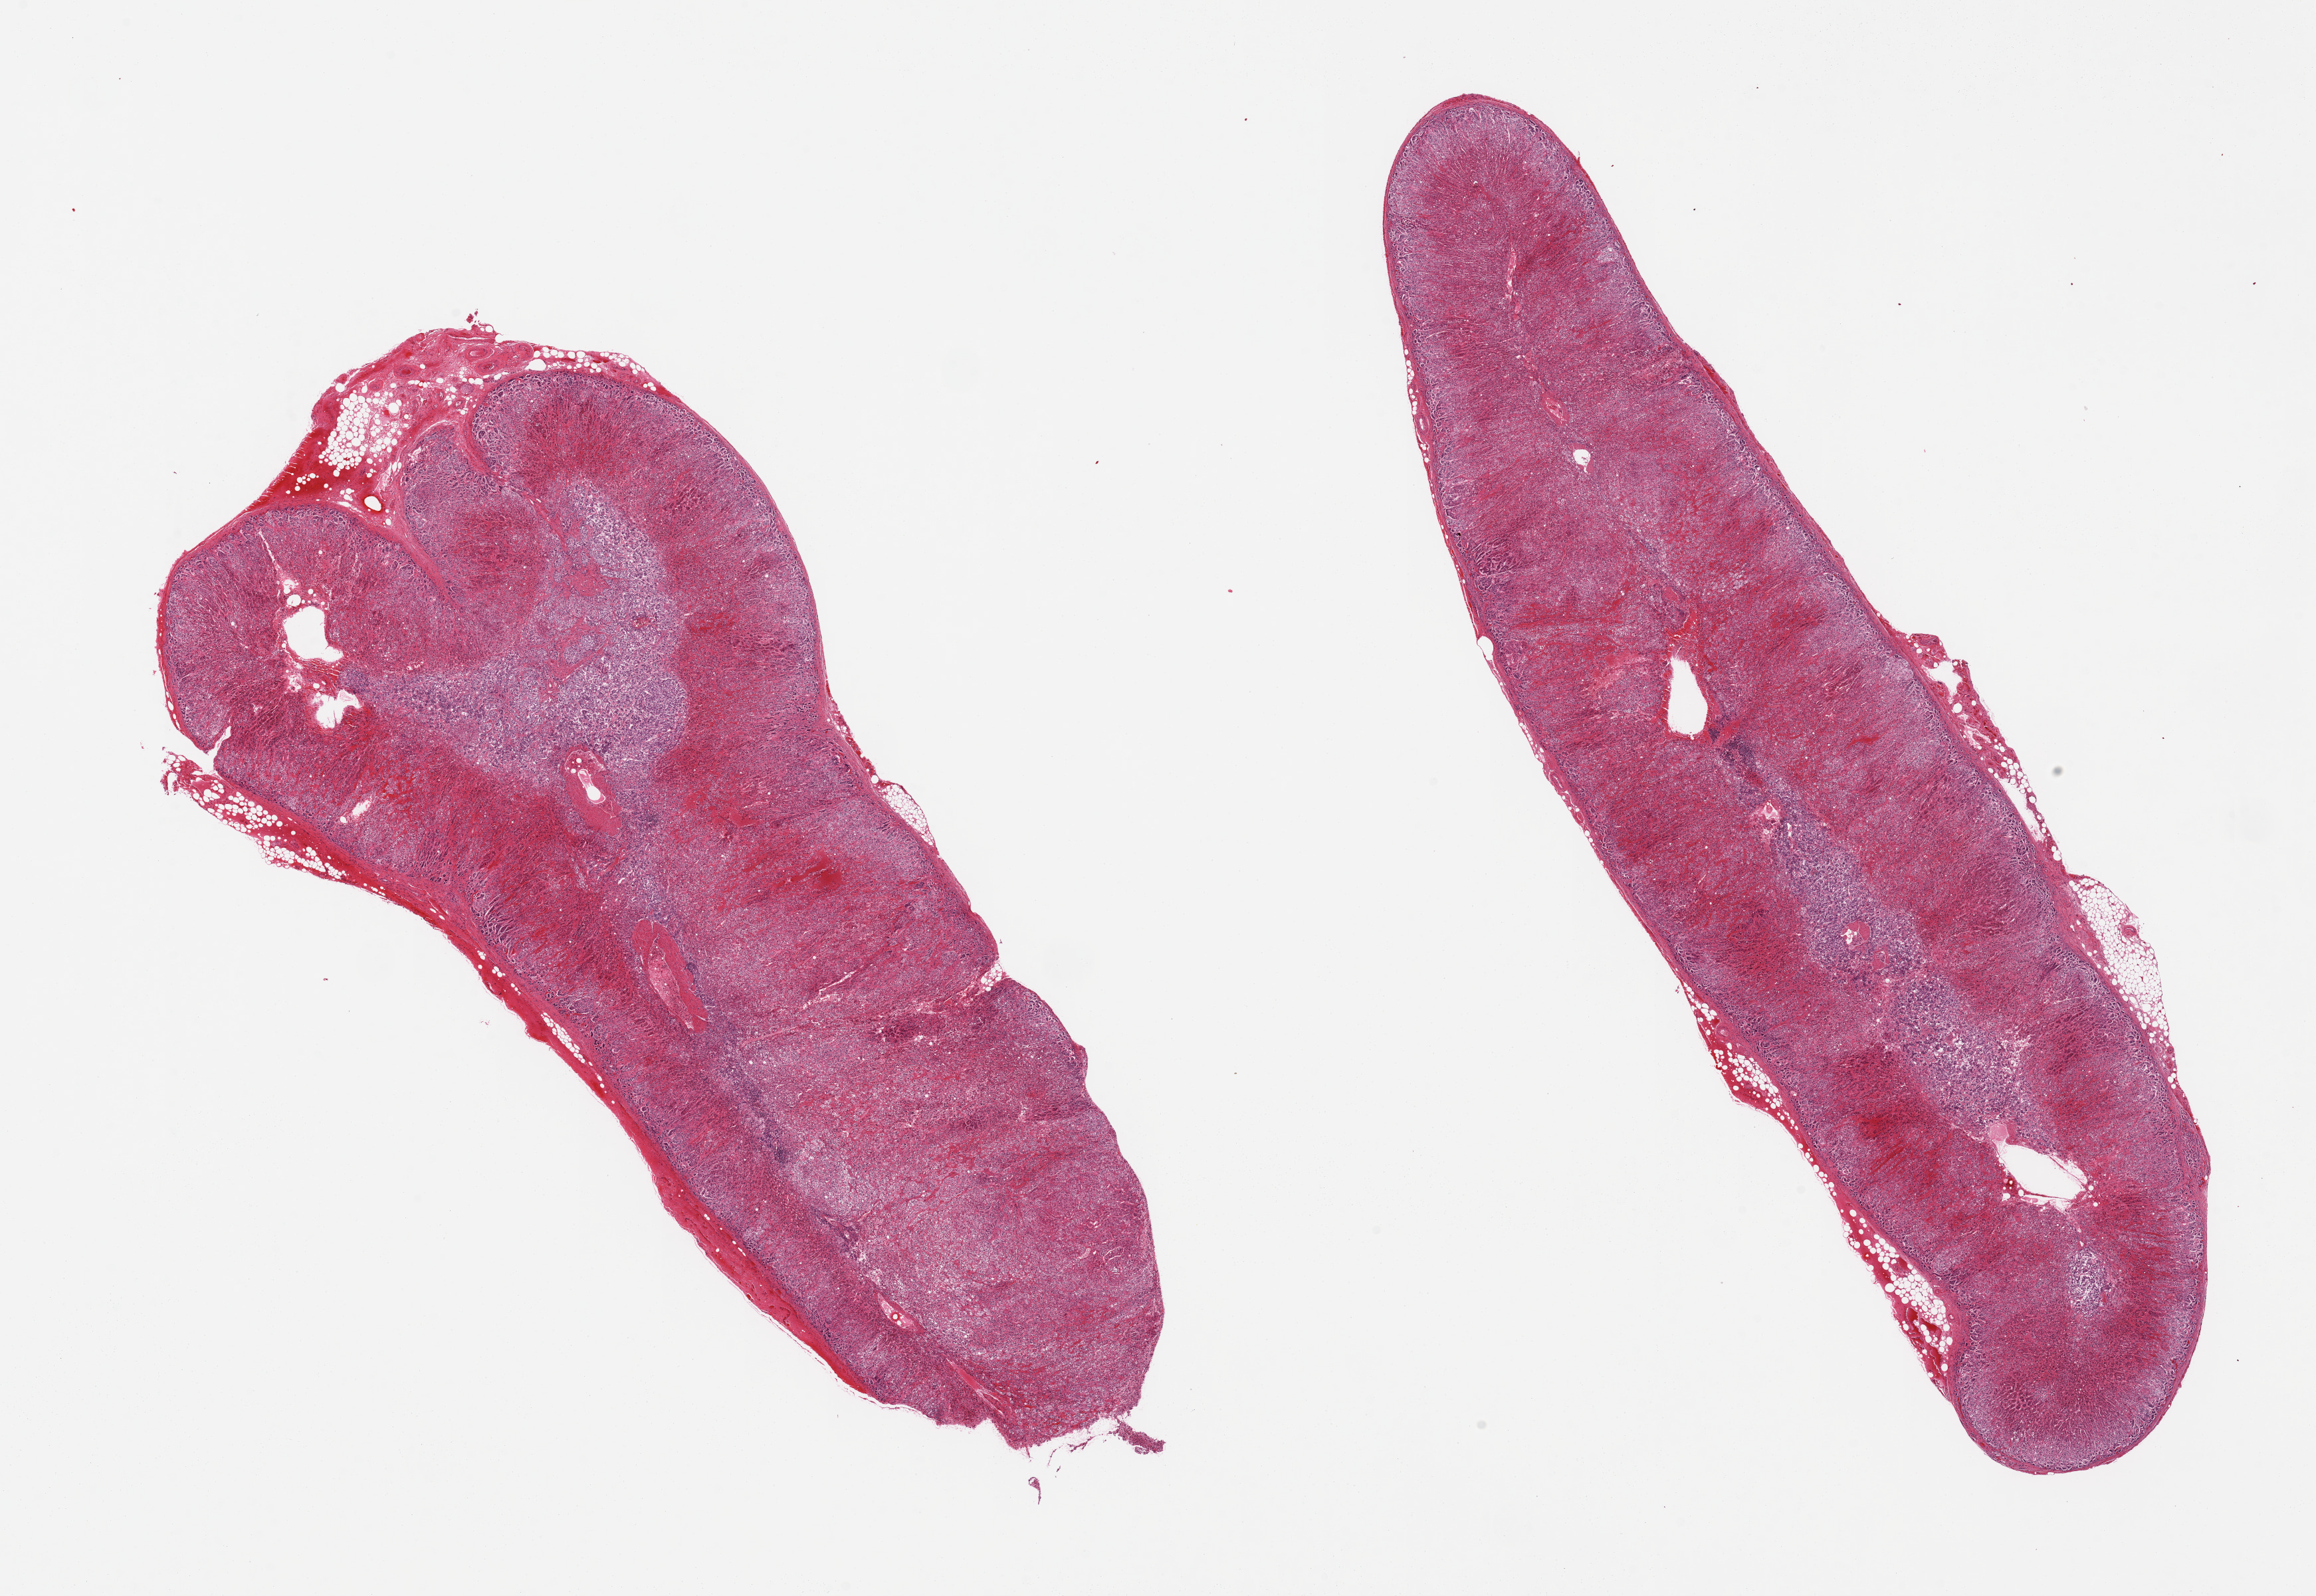
Digitized hematoxylin and eosin (H&E)-stained section, brightfield — whole scanned area (about 27.6 x 19.0 mm, from a 20x scan) shown as a low-resolution overview. PAXgene-fixed paraffin-embedded (PFPE) section. Sampled site (target tissue): adrenal gland. Tissue donor sample. Female donor.
- reviewer comment on this tissue sample: 2 pieces, well preserved; abundant cortex and medulla visible in both sections--valuable specimen